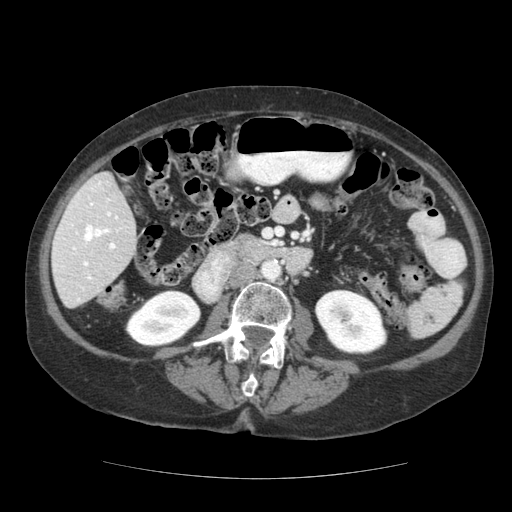
Contrast-enhanced abdominal CT (liver protocol), one axial slice. Reconstruction kernel STANDARD. Soft-tissue window (W 400 / L 40 HU). 2.5 mm slice thickness. 512 × 512 image matrix. Case-level facts recorded for this patient, not image findings: diagnosis: hepatocellular carcinoma (patient treated with transarterial chemoembolisation; whether this scan precedes or follows treatment is not stated here); TNM stage (as recorded): Stage-I; Child-Pugh class: A; tumour differentiation: moderately-poorly differentiated; tumour size: 7.3 cm.
Annotated regions visible in this slice (semi-automatically segmented with operator editing):
- liver parenchyma outside the tumour (the mass and vessels are separate outlines, so this box may not span the whole liver): box from (x=52, y=172) to (x=136, y=307) px
- liver vessels: (x=54, y=181)–(x=118, y=301)